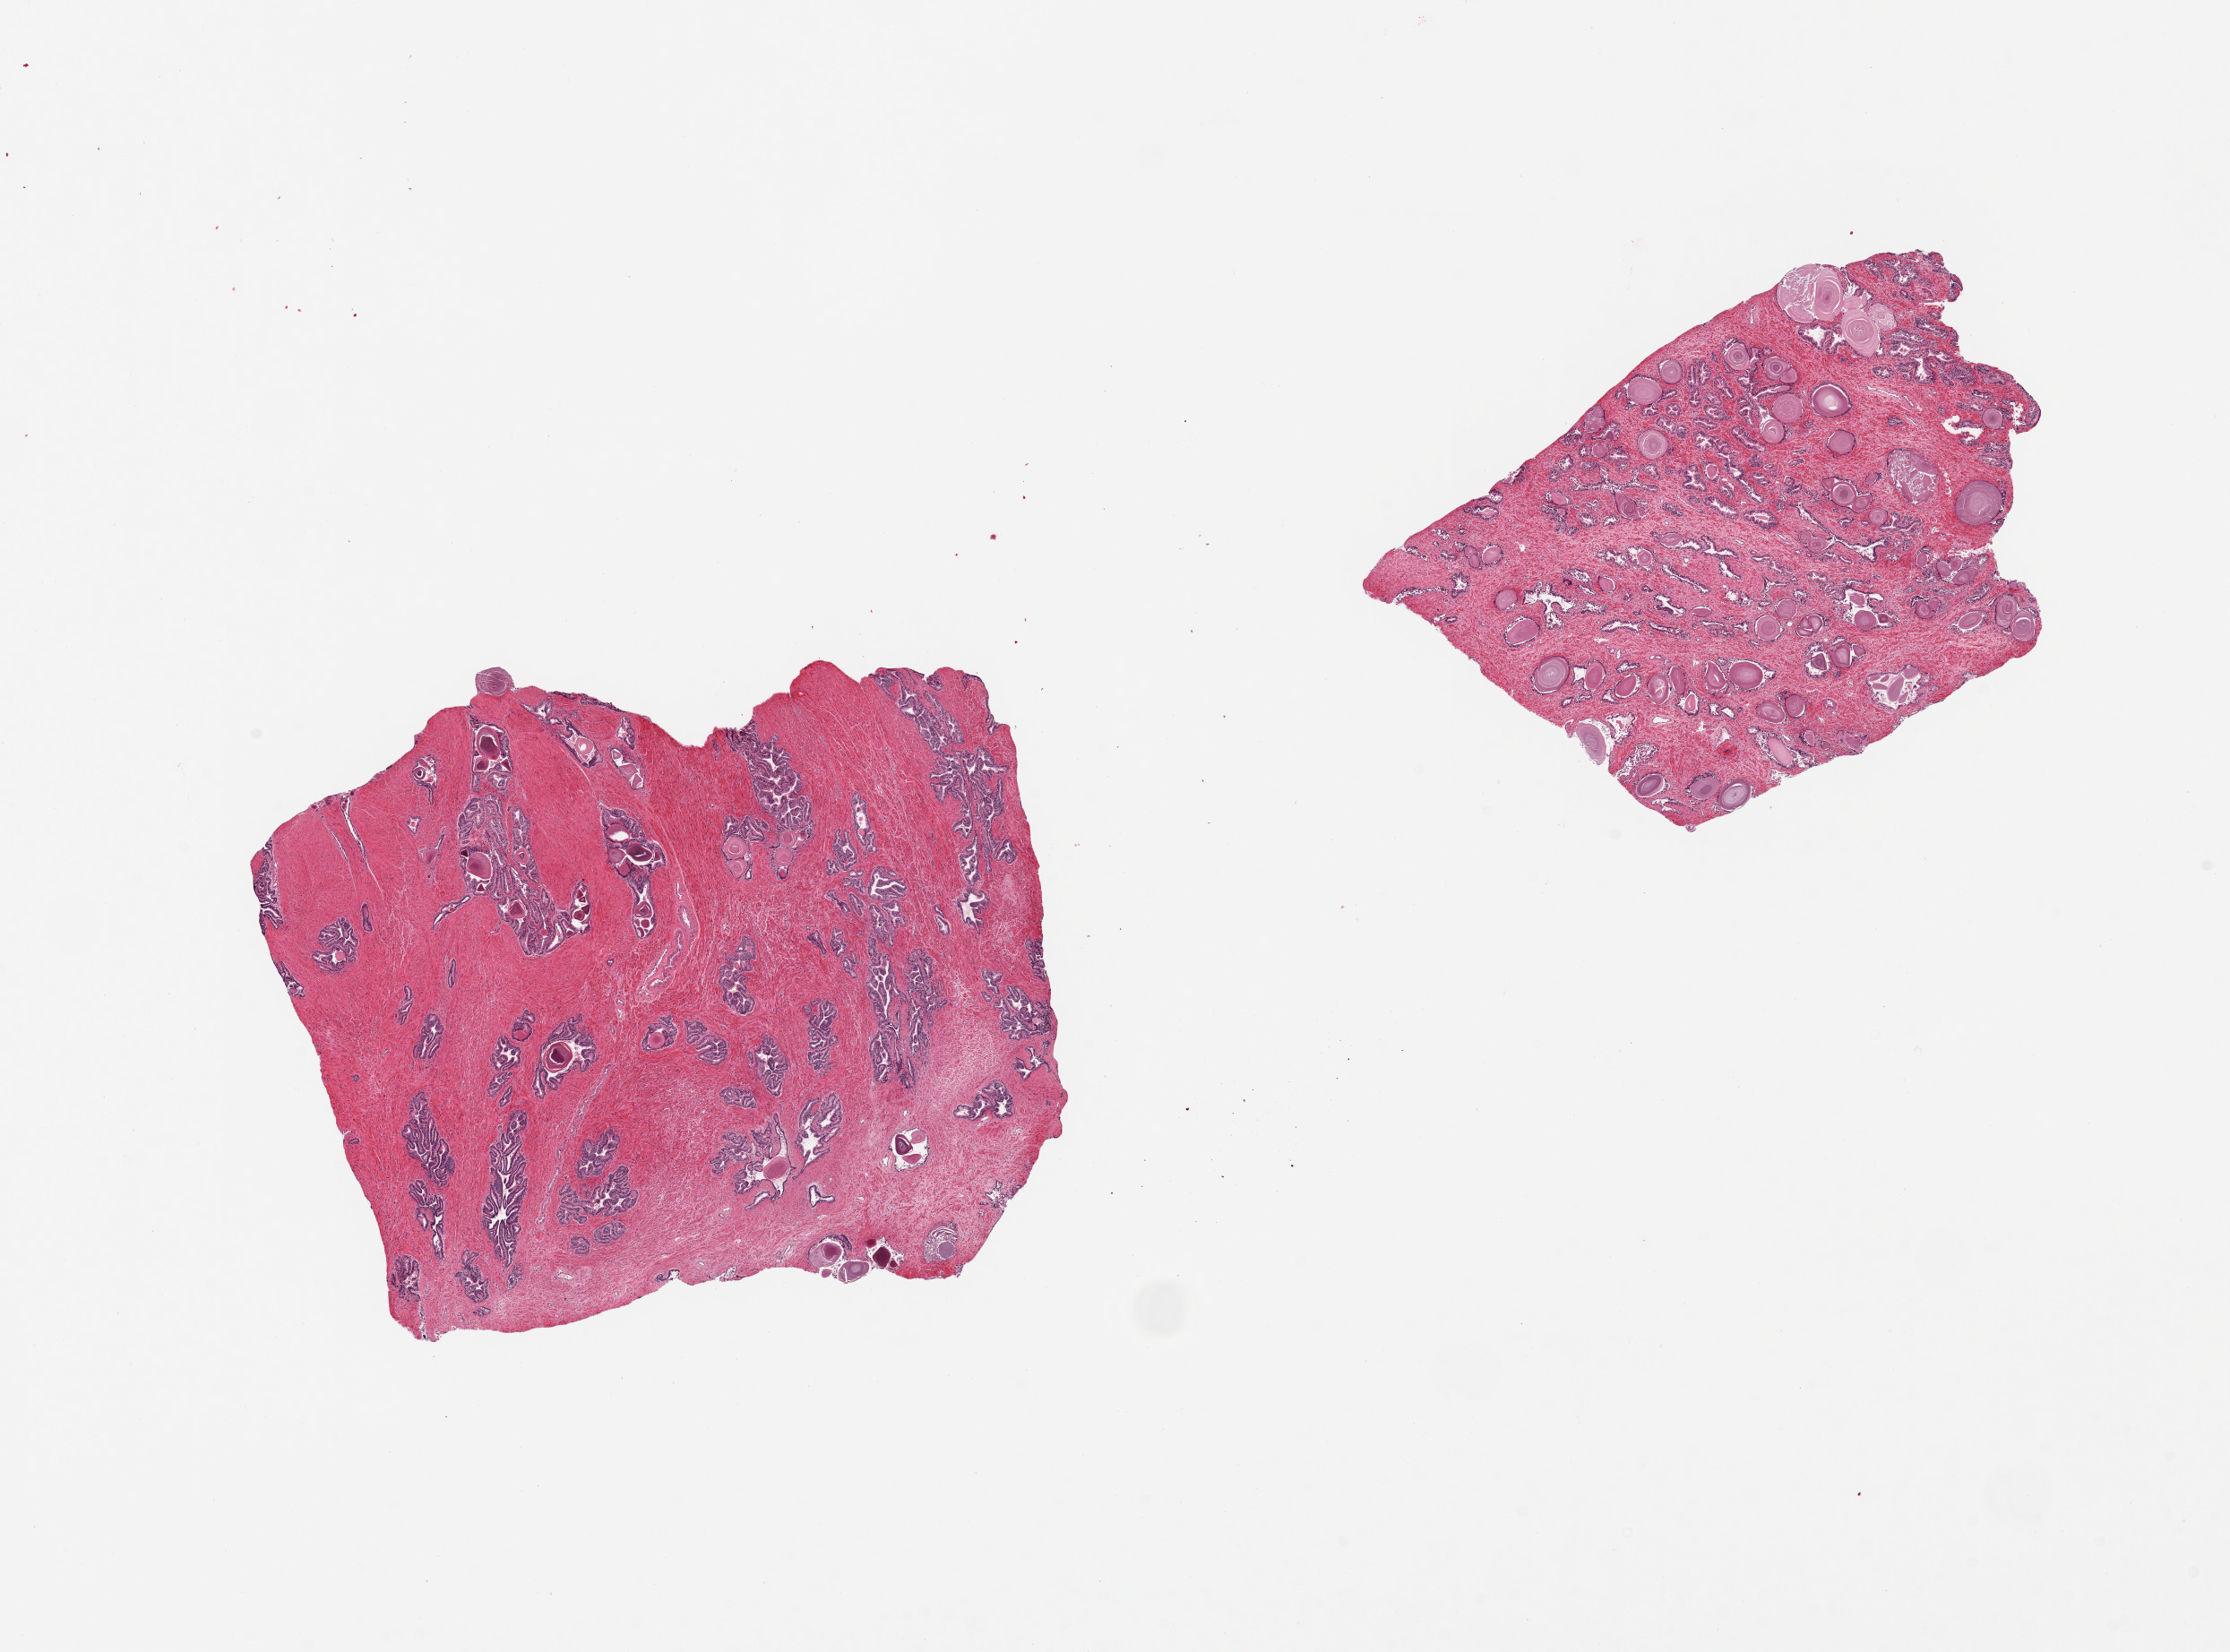
Digitized H&E-stained section — whole scanned area (about 19.7 x 14.6 mm) shown as a low-resolution overview; PAXgene-fixed paraffin-embedded (PFPE) section; sampled site (target tissue): prostate; donor tissue sample. Donor sex: male.
Pathologist's review note for this sample: 2 pieces, glandular hyperplasia; some foci approach autolysis score 2.